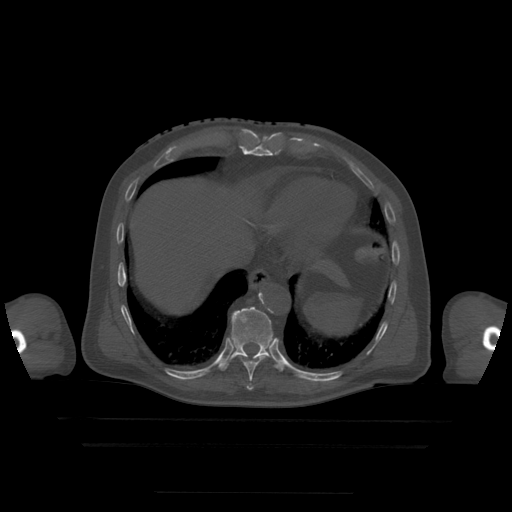
CT including the spine, one axial slice; slice 250 of 522 in the series (ordered by position); bone window (W 1800 / L 400 HU); 1.25 mm slice thickness; 512 × 512 image matrix. Patient age 68 years. From the clinical record (not read from this slice): primary cancer: urothelial.
Outlined on this slice (semi-automatic segmentation, software-assisted and operator-edited):
- T10 vertebra: bounding box [x1, y1, x2, y2] px = [221, 307, 284, 372]
- T9 vertebra: [243, 356, 266, 391]